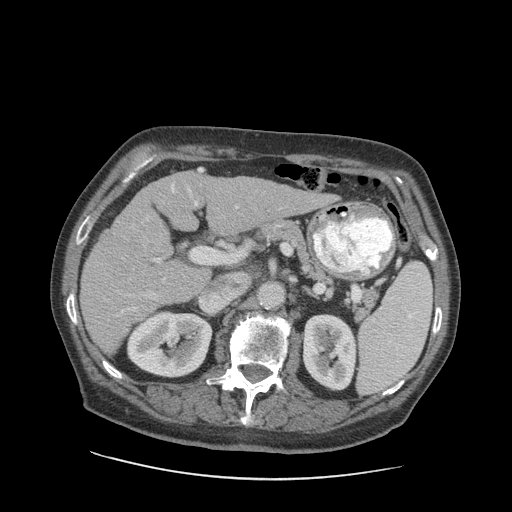
Contrast-enhanced abdominal CT (liver protocol), one axial slice; position 47 of 89 along the scan axis; 140 kVp; soft-tissue window (W 400 / L 40 HU); 2.5 mm slice thickness; 512 × 512 image matrix. From the clinical record (not read from this slice): diagnosis: hepatocellular carcinoma (patient treated with transarterial chemoembolisation; whether this scan precedes or follows treatment is not stated here); TNM stage (as recorded): Stage-I; Child-Pugh class: A; tumour differentiation: moderately differentiated; tumour nodularity: uninodular.
Outlined on this slice (semi-automatically segmented with operator editing):
- liver parenchyma outside the tumour (the mass and vessels are separate outlines, so this box may not span the whole liver): bounding box (x1, y1, x2, y2) in pixels: (80, 168, 328, 354)
- mass: (127, 215, 172, 257)
- liver vessels: (104, 169, 282, 317)